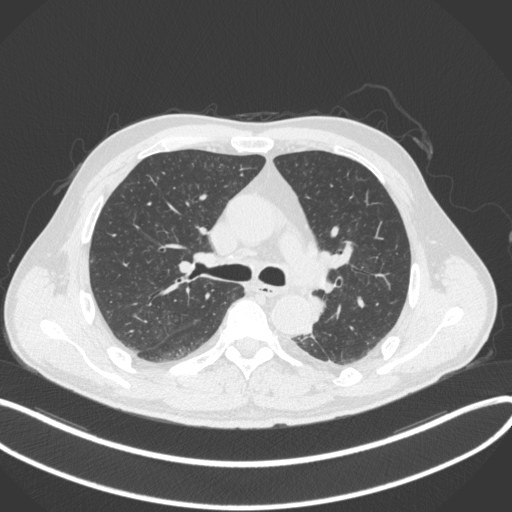
Chest CT, one axial slice. Position 223 of 328 along the scan axis. Lung window (W 1500 / L -600 HU). 1 mm slice thickness. 512 × 512 image matrix. Patient: male, 59 years. Case-level facts recorded for this patient, not image findings: clinical TNM (as recorded): T2a N2 M0.
Annotated regions visible in this slice (bounding box drawn by a radiologist):
- lung tumour (recorded histology: squamous cell carcinoma): bounding box [x1, y1, x2, y2] px = [306, 295, 330, 324]